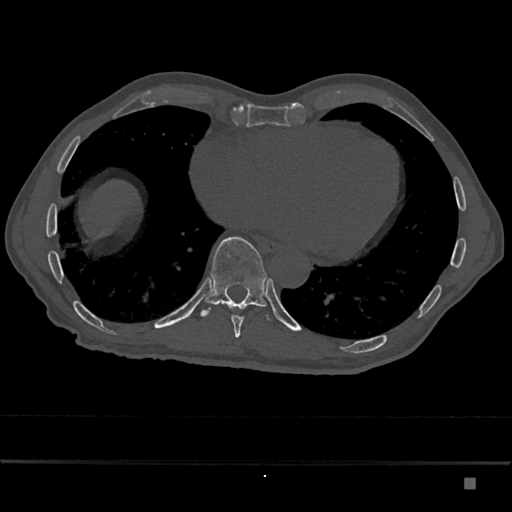
CT including the spine, one axial slice. Position 766 of 797 along the scan axis. Reconstruction kernel Br40s/3. Bone window (W 1800 / L 400 HU). 0.5 mm slice thickness. 512 × 512 image matrix. Patient: male, 72 years. Case-level facts recorded for this patient, not image findings: primary cancer: prostate.
Structures marked on this image (semi-automatically segmented with operator editing):
- T10 vertebra: box from (x=200, y=237) to (x=272, y=321) px
- T9 vertebra: (x=231, y=315)–(x=244, y=338)